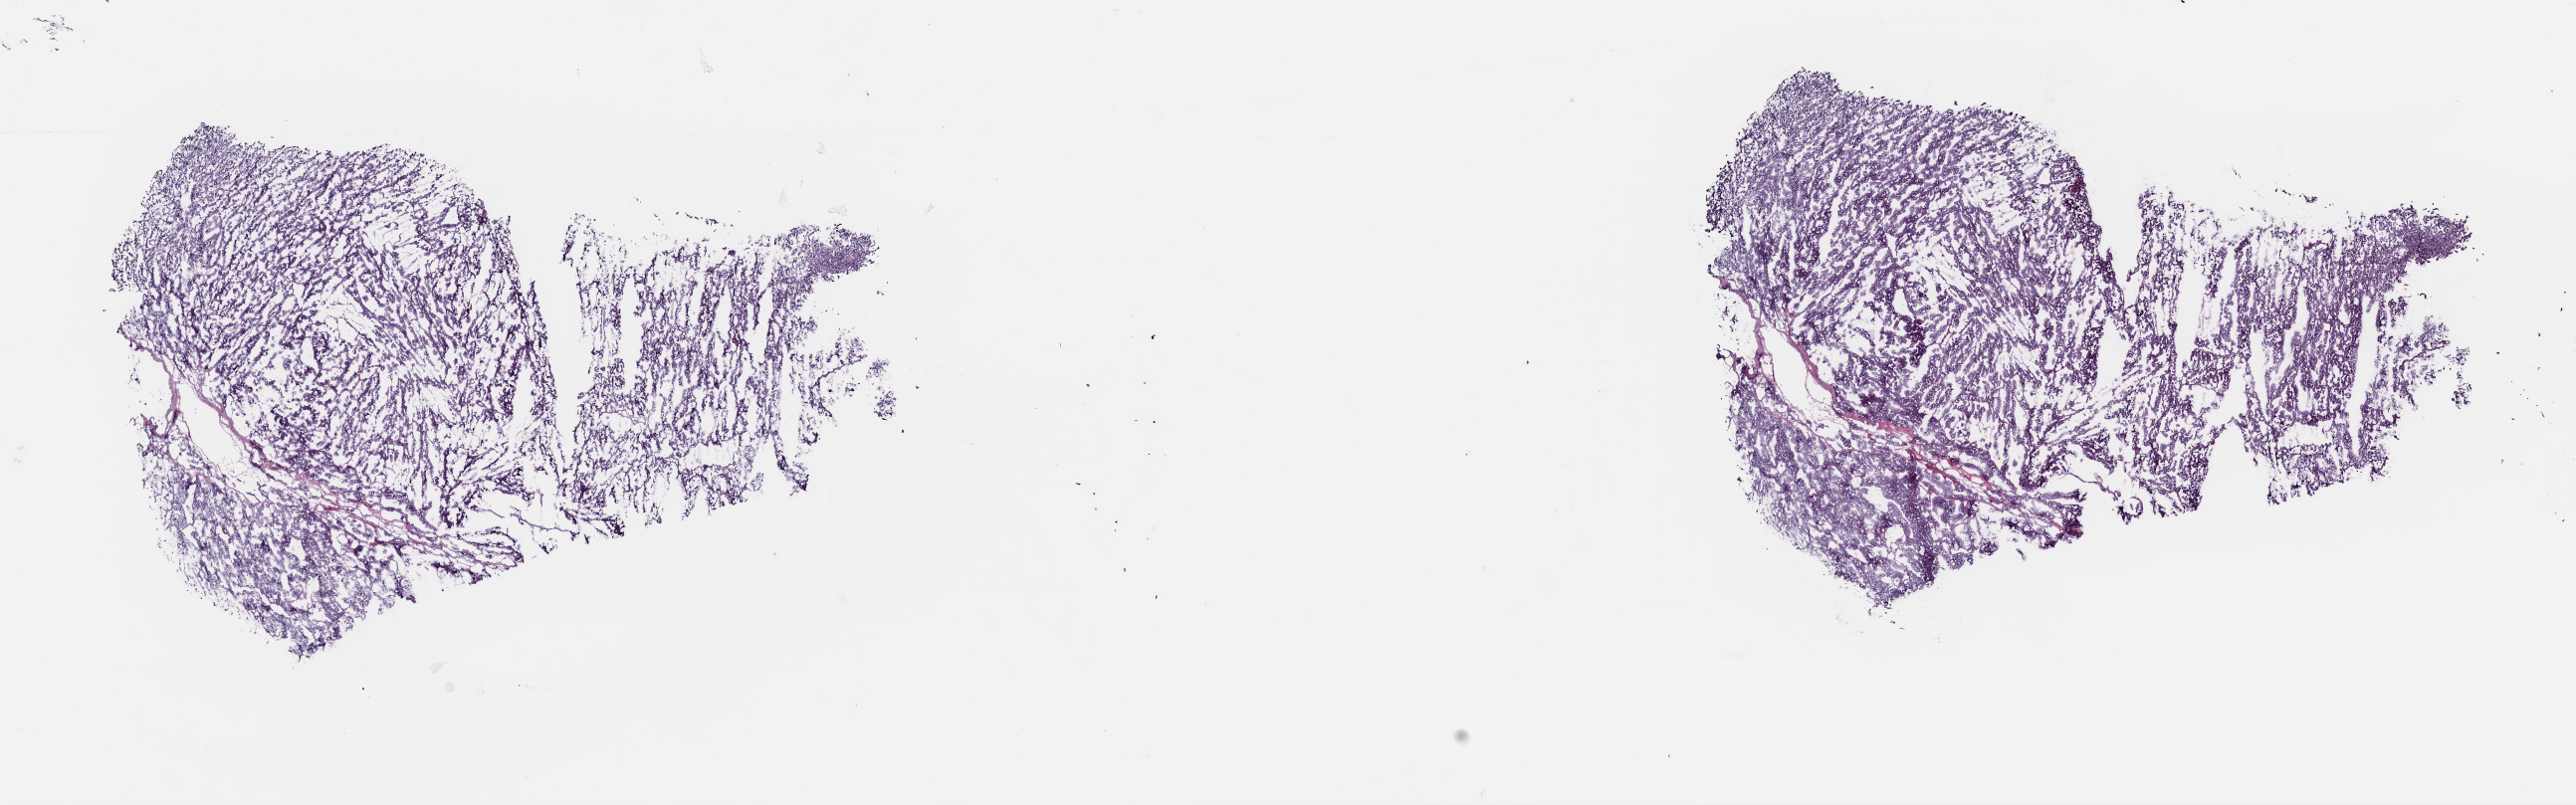
H&E whole-slide image — shown as a low-resolution overview of the whole scanned area (about 20.4 x 6.4 mm, acquisition: 40x scan). Frozen section. Adrenal cortex, primary tumour sample. Female, age 36 years at initial diagnosis. Pathologist review of this section (percent, as recorded): tumour cells 95%, tumour nuclei 95%, normal cells 0%, stromal cells 5%, necrosis 0%. Inflammatory infiltration, as recorded: lymphocyte infiltration 20%, monocyte infiltration 20%, neutrophil infiltration 40%.
Laterality: left. Diagnosis: Adrenal cortical carcinoma (cortex of adrenal gland).